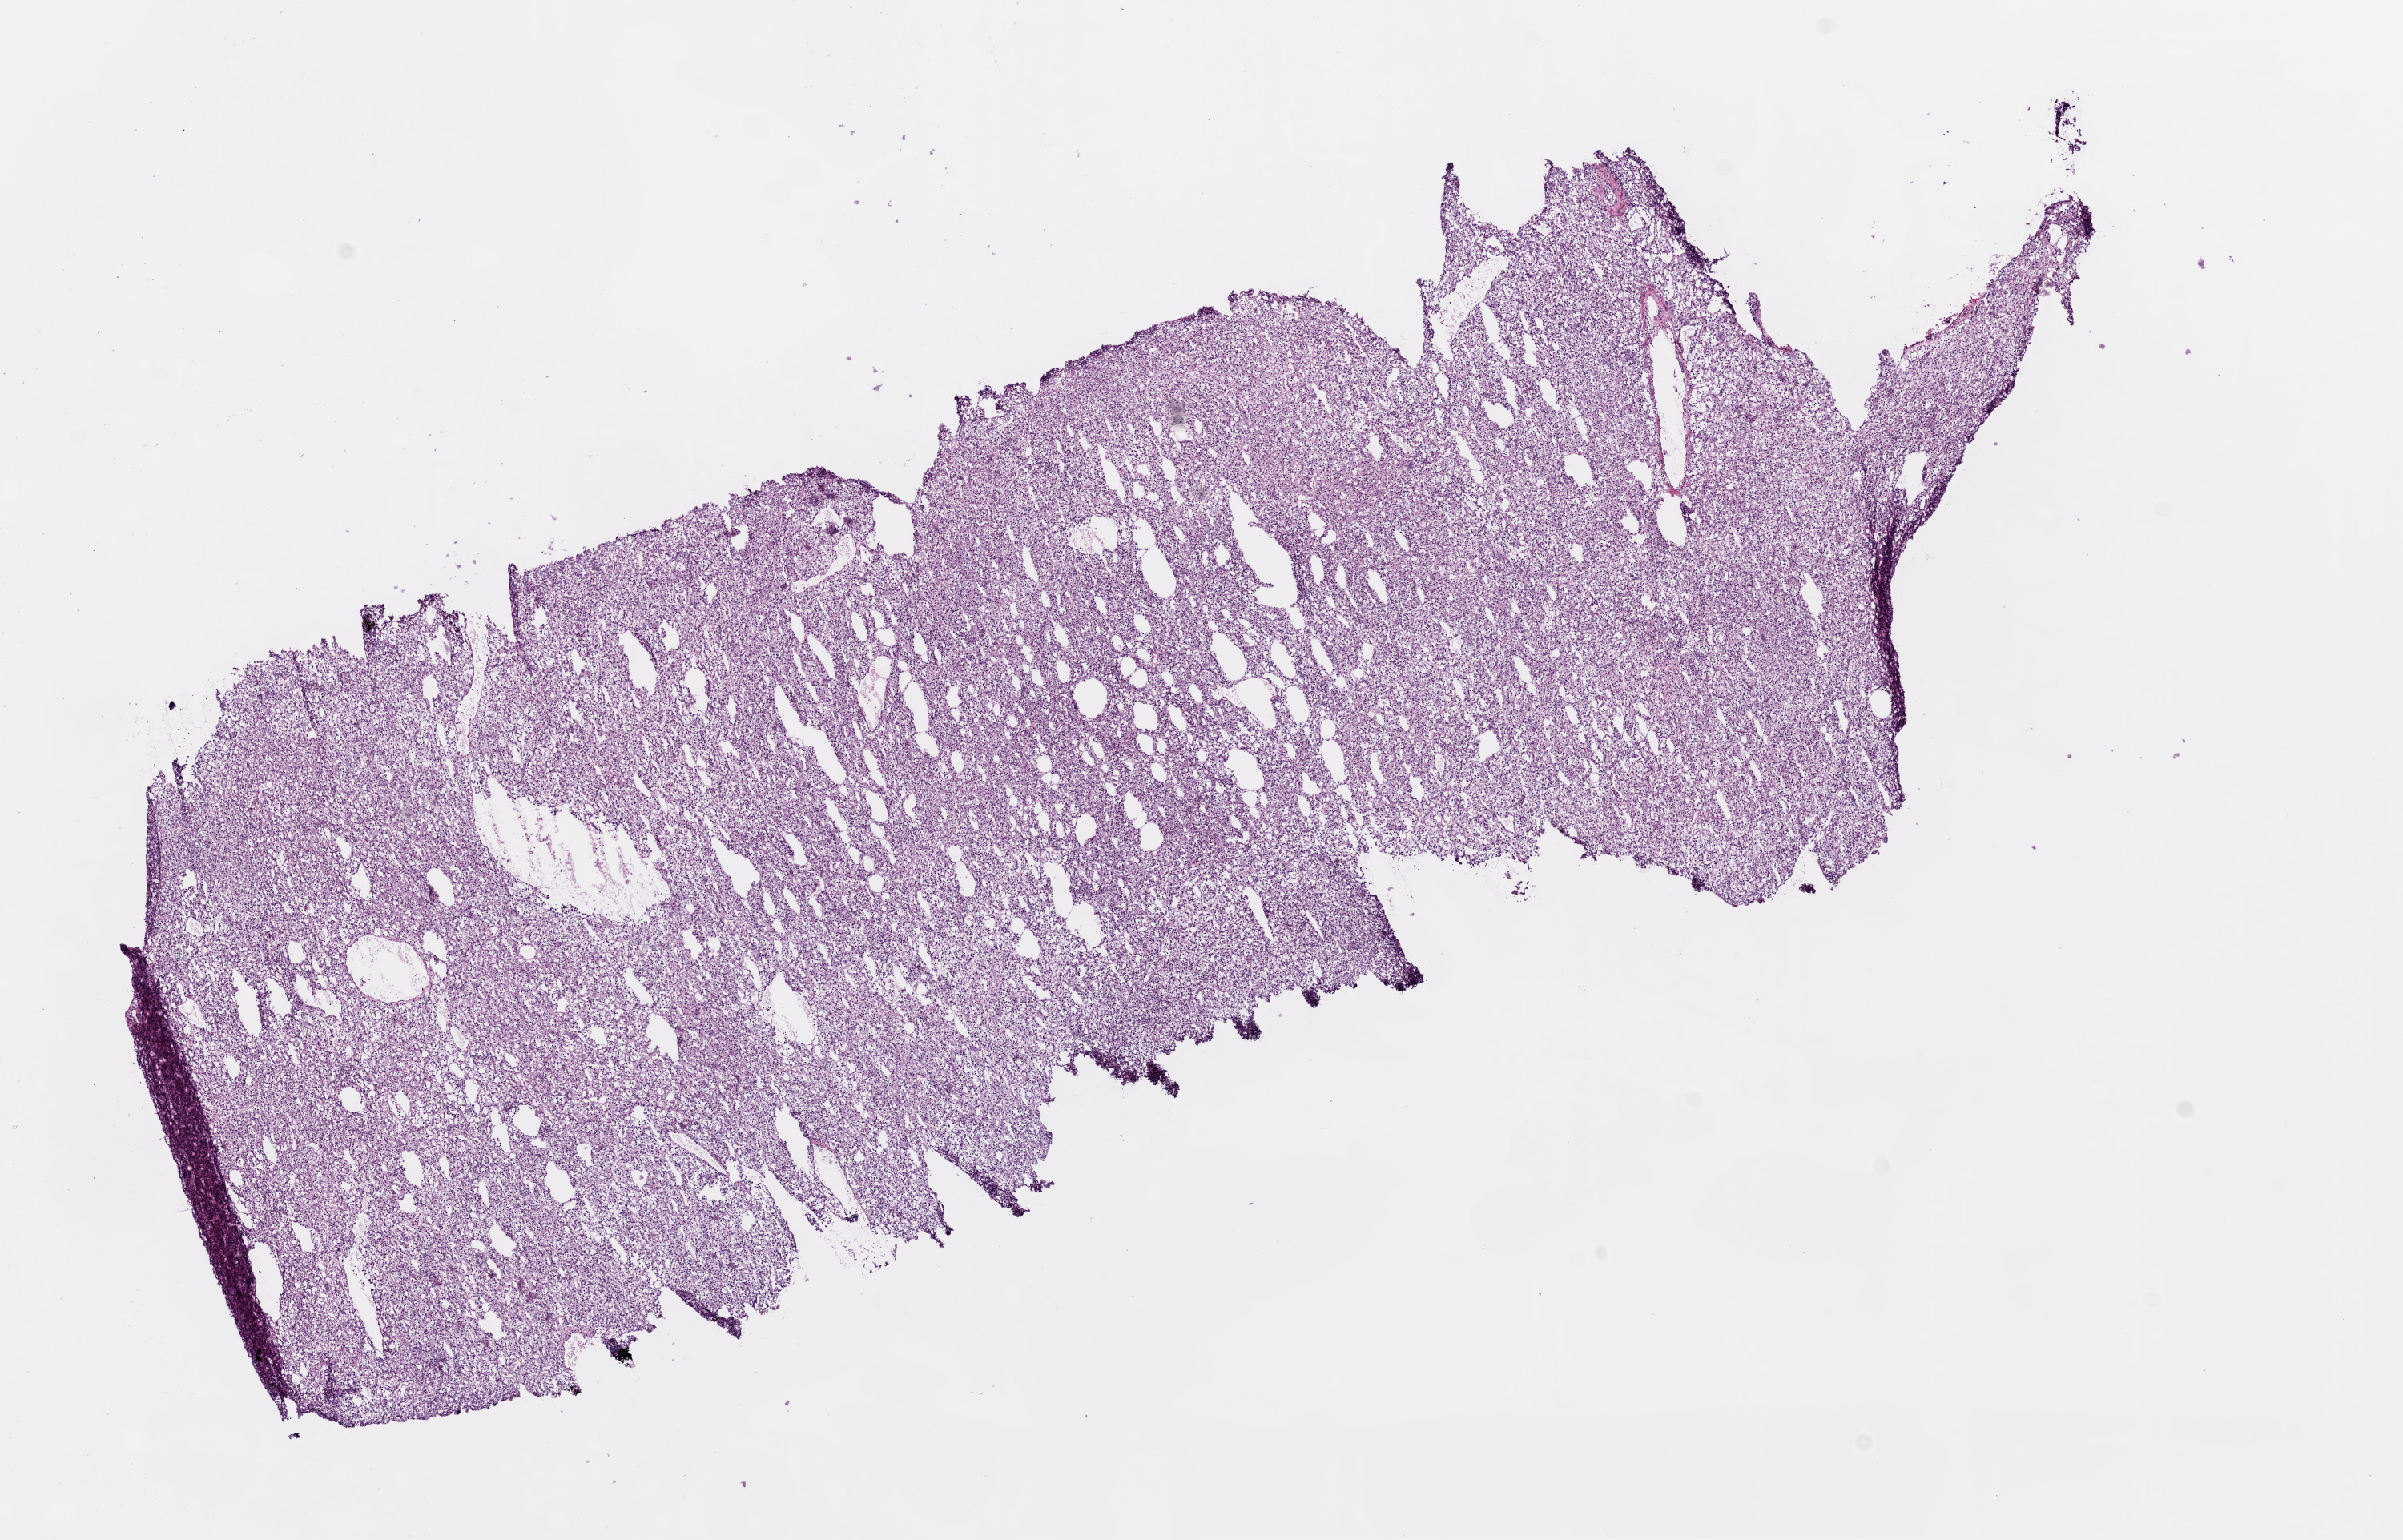
Digitized Hematoxylin and eosin (H&E) stained tissue section (whole slide), shown as a low-resolution overview of the whole scanned area (about 12.0 x 7.7 mm); frozen section; primary tumour sample from the kidney. Male patient; age at initial diagnosis 47 years. Histologic grade: G1 (well differentiated). Pathologist review of this section (percent, as recorded): tumour cells 95%, tumour nuclei 85%, normal cells 0%, stromal cells 5%, necrosis 0%.
AJCC pathologic stage: I. Laterality: right. Diagnosis: Clear cell adenocarcinoma, NOS. TNM: T1a NX M0.